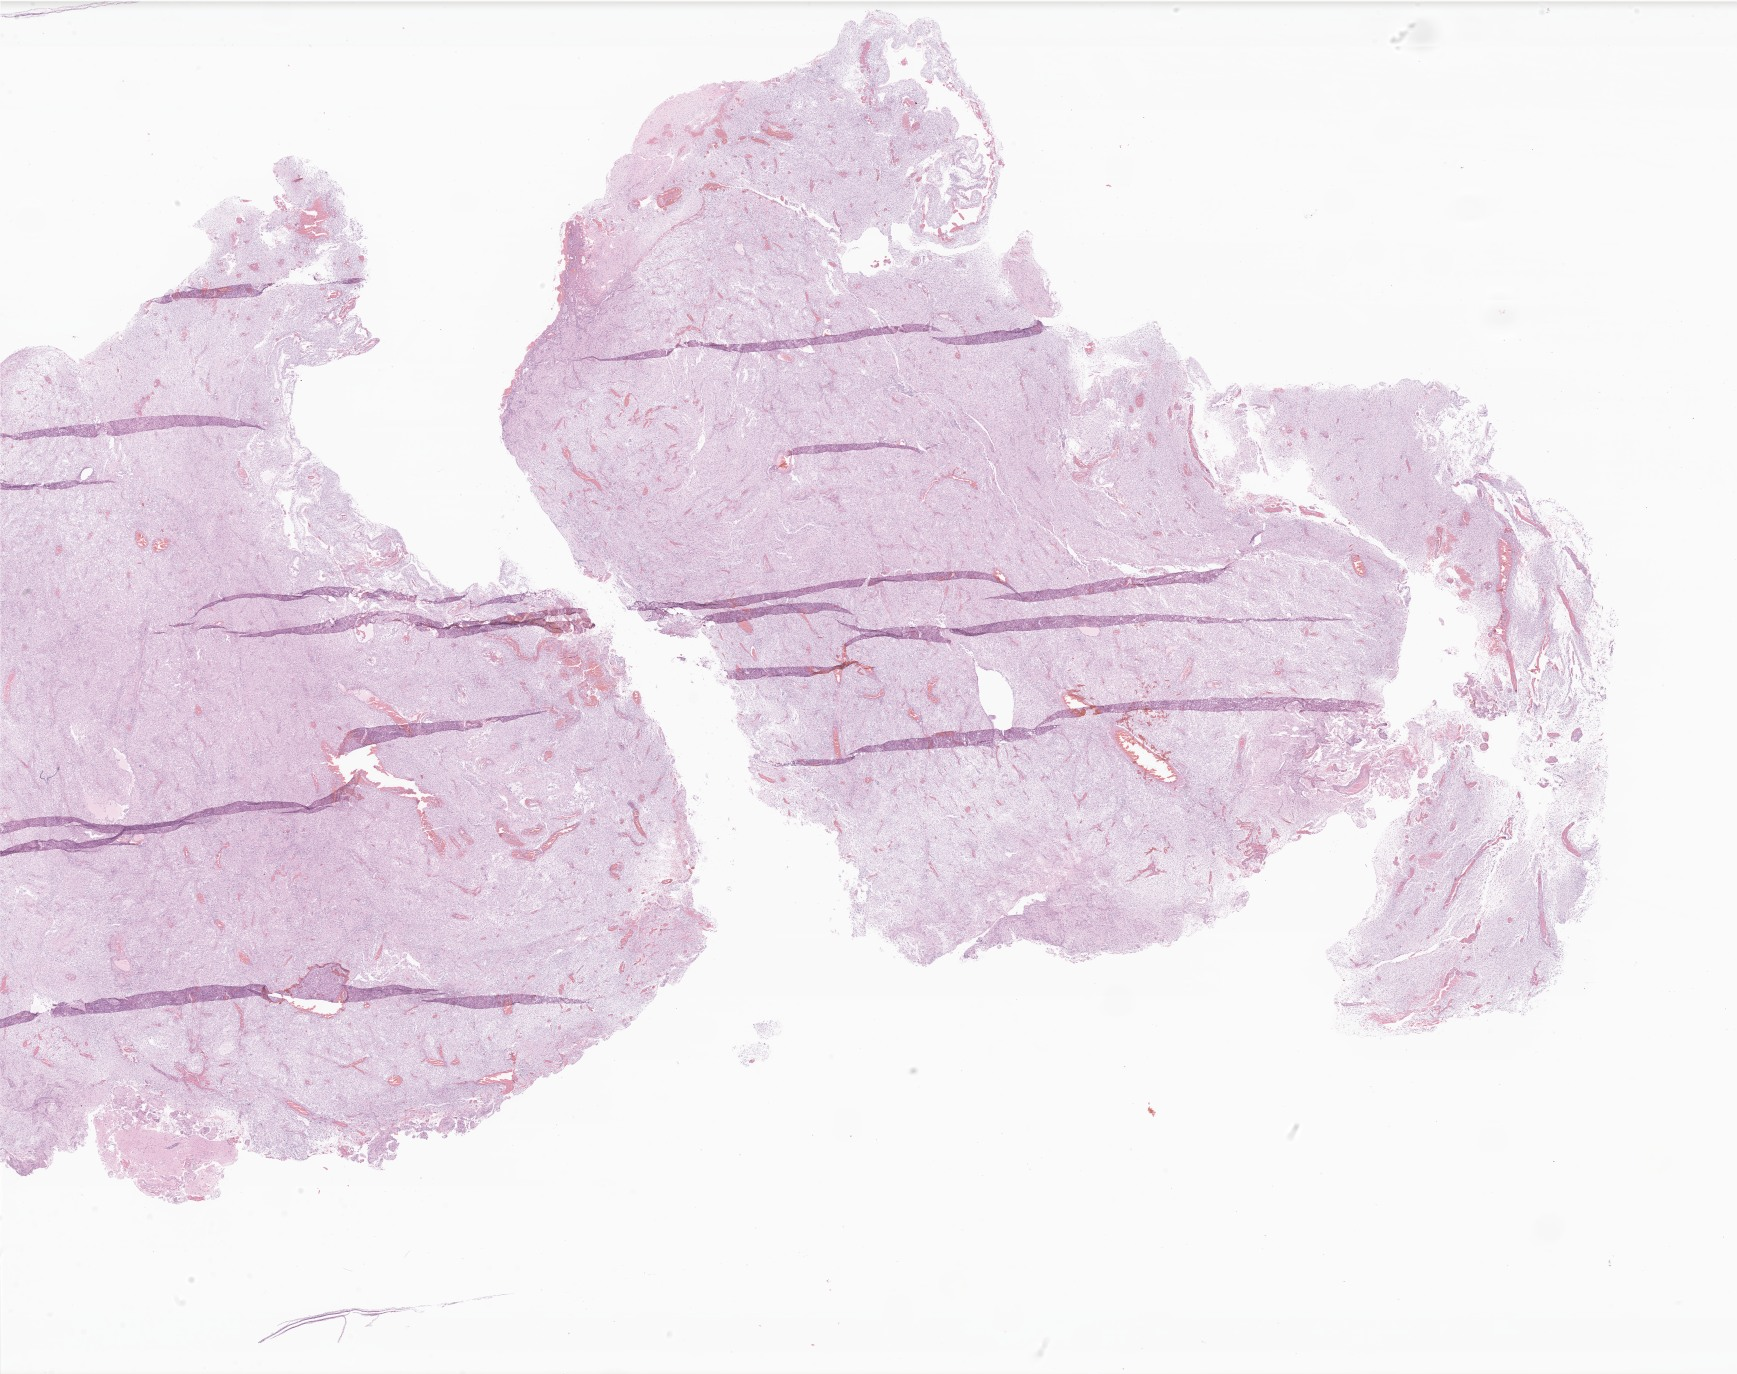
H&E whole-slide image of tumor tissue from the brain, shown as a low-resolution overview of the whole scanned area (about 29.3 x 23.2 mm), FFPE section. Patient: male, age 34 months (2 years 10 months).
Recorded diagnosis: Pilocytic astrocytoma.